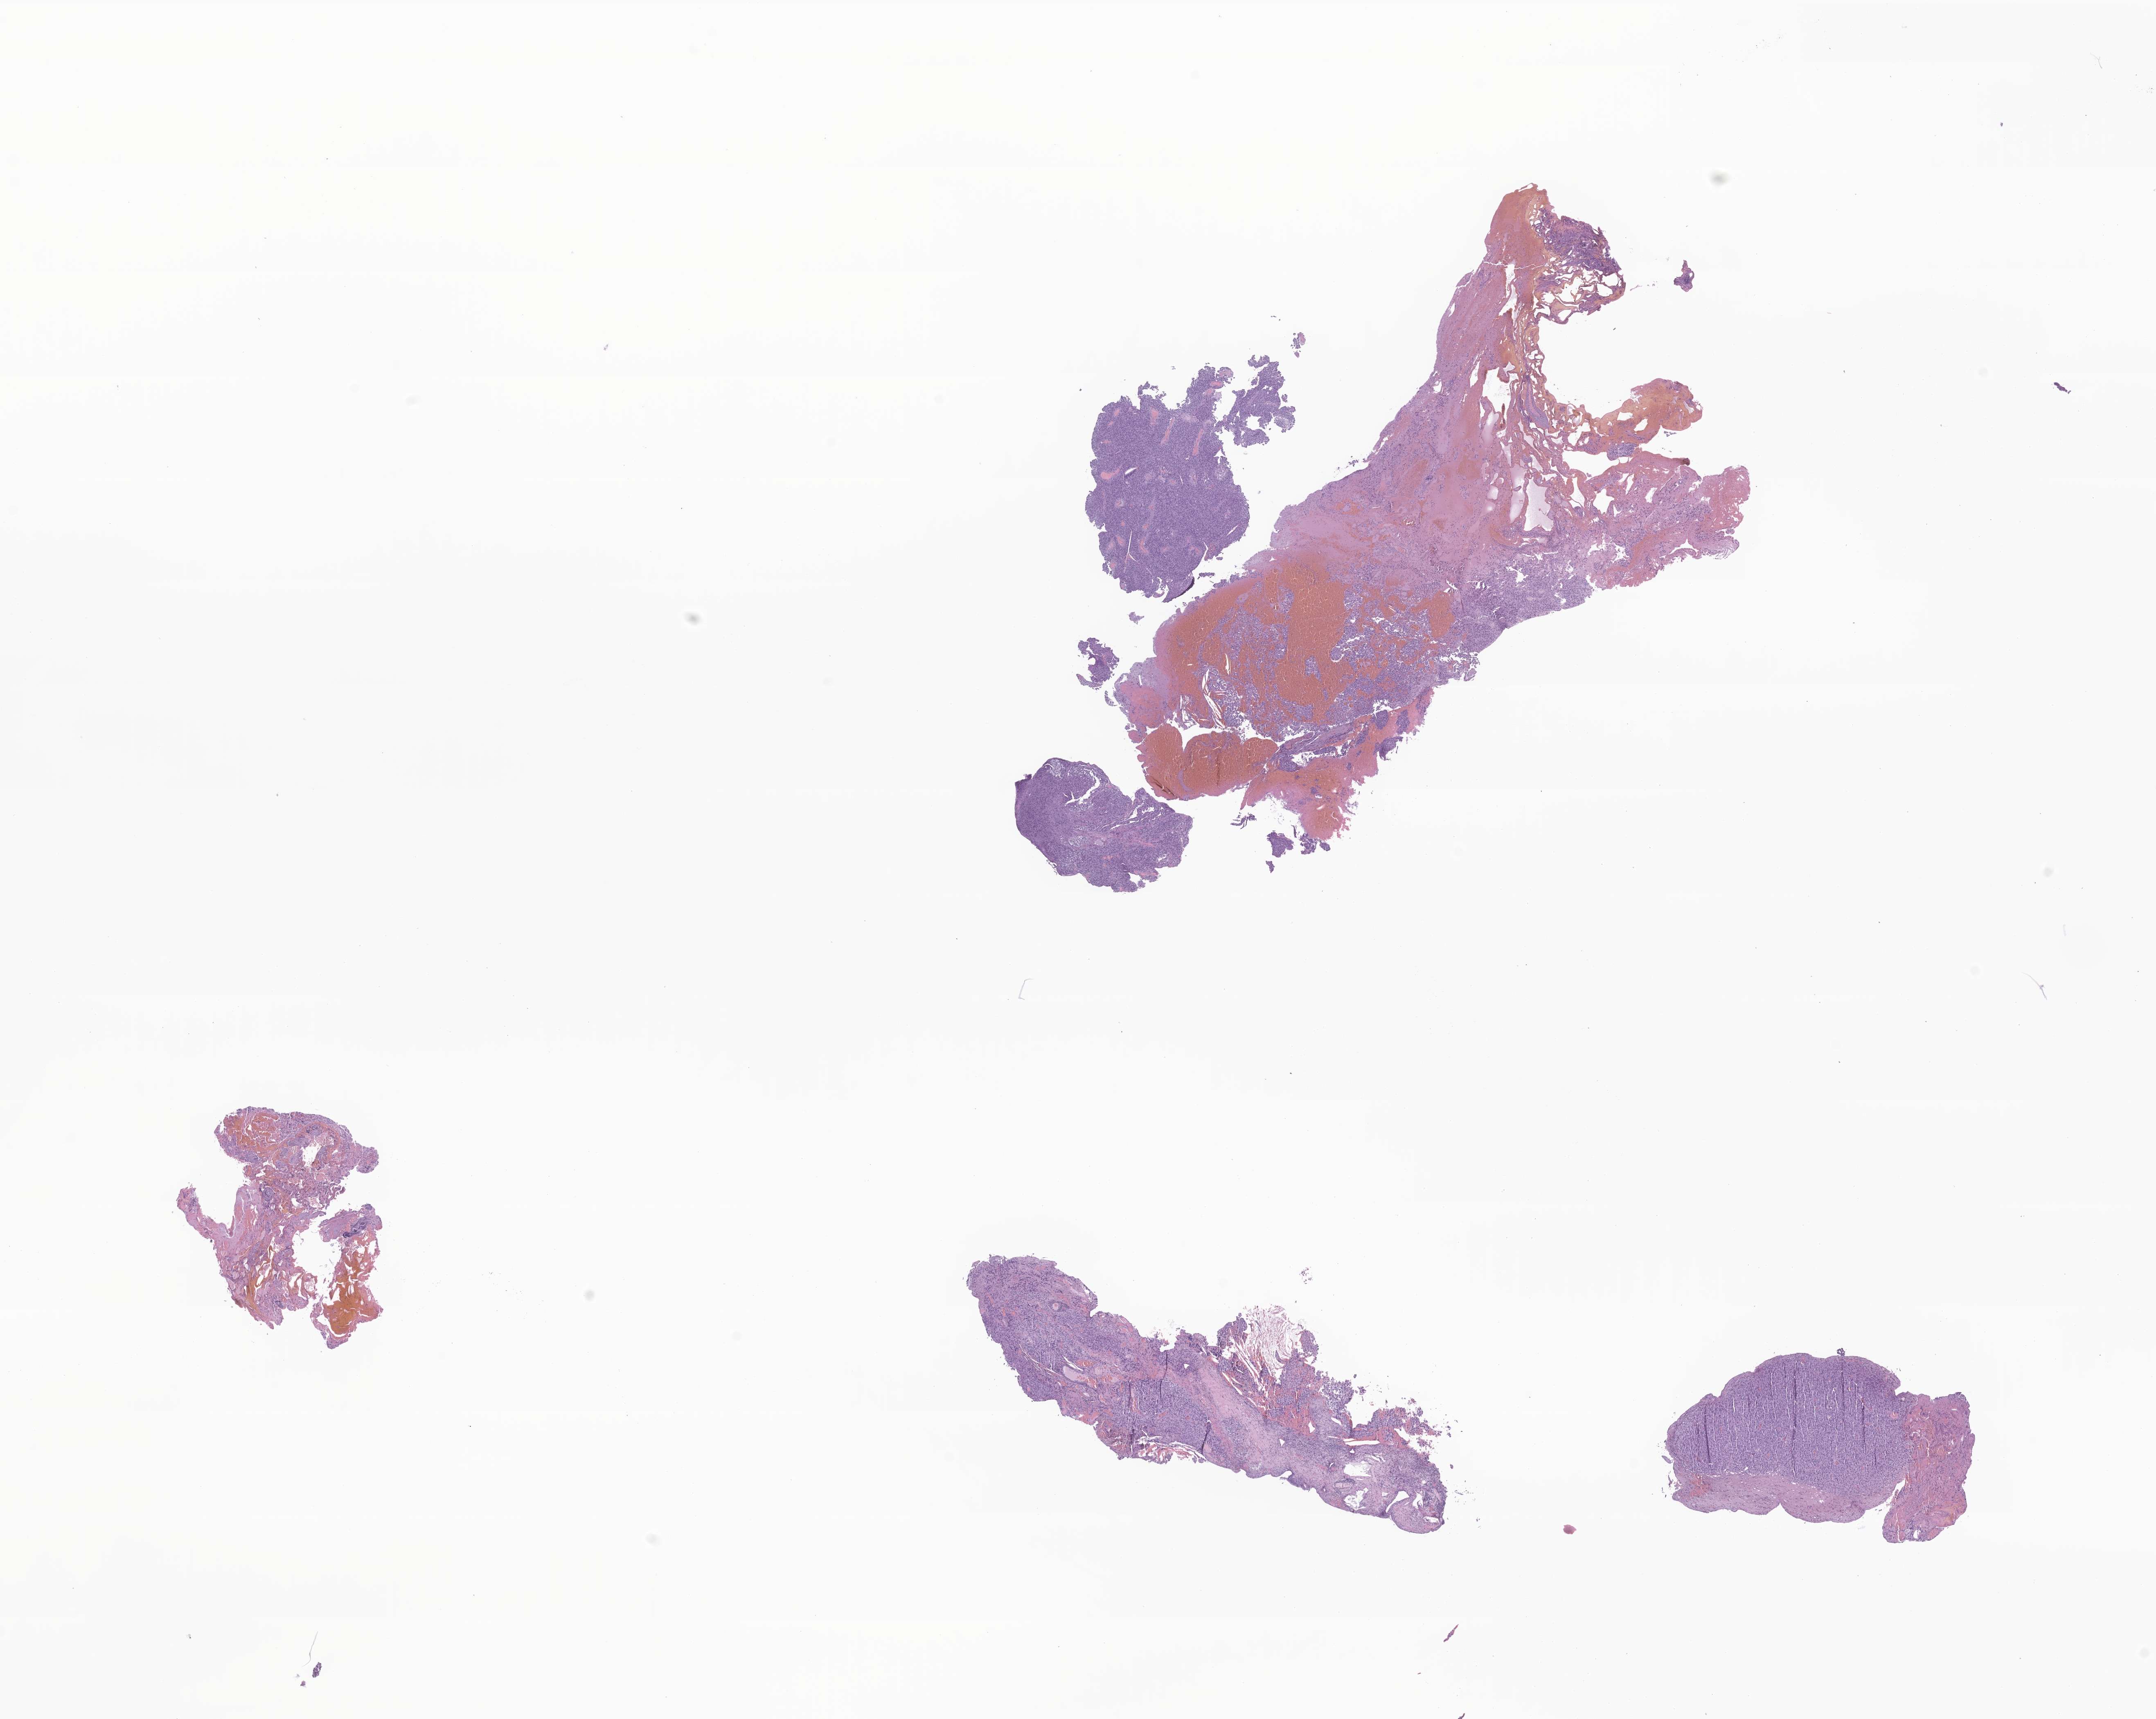
Digitized H&E-stained section of tumor tissue from the brain — low-resolution overview of the scanned area, about 22.2 x 17.7 mm; formalin-fixed paraffin-embedded section. Female patient, age 216 months (18 years).
* recorded diagnosis: Glioma, malignant